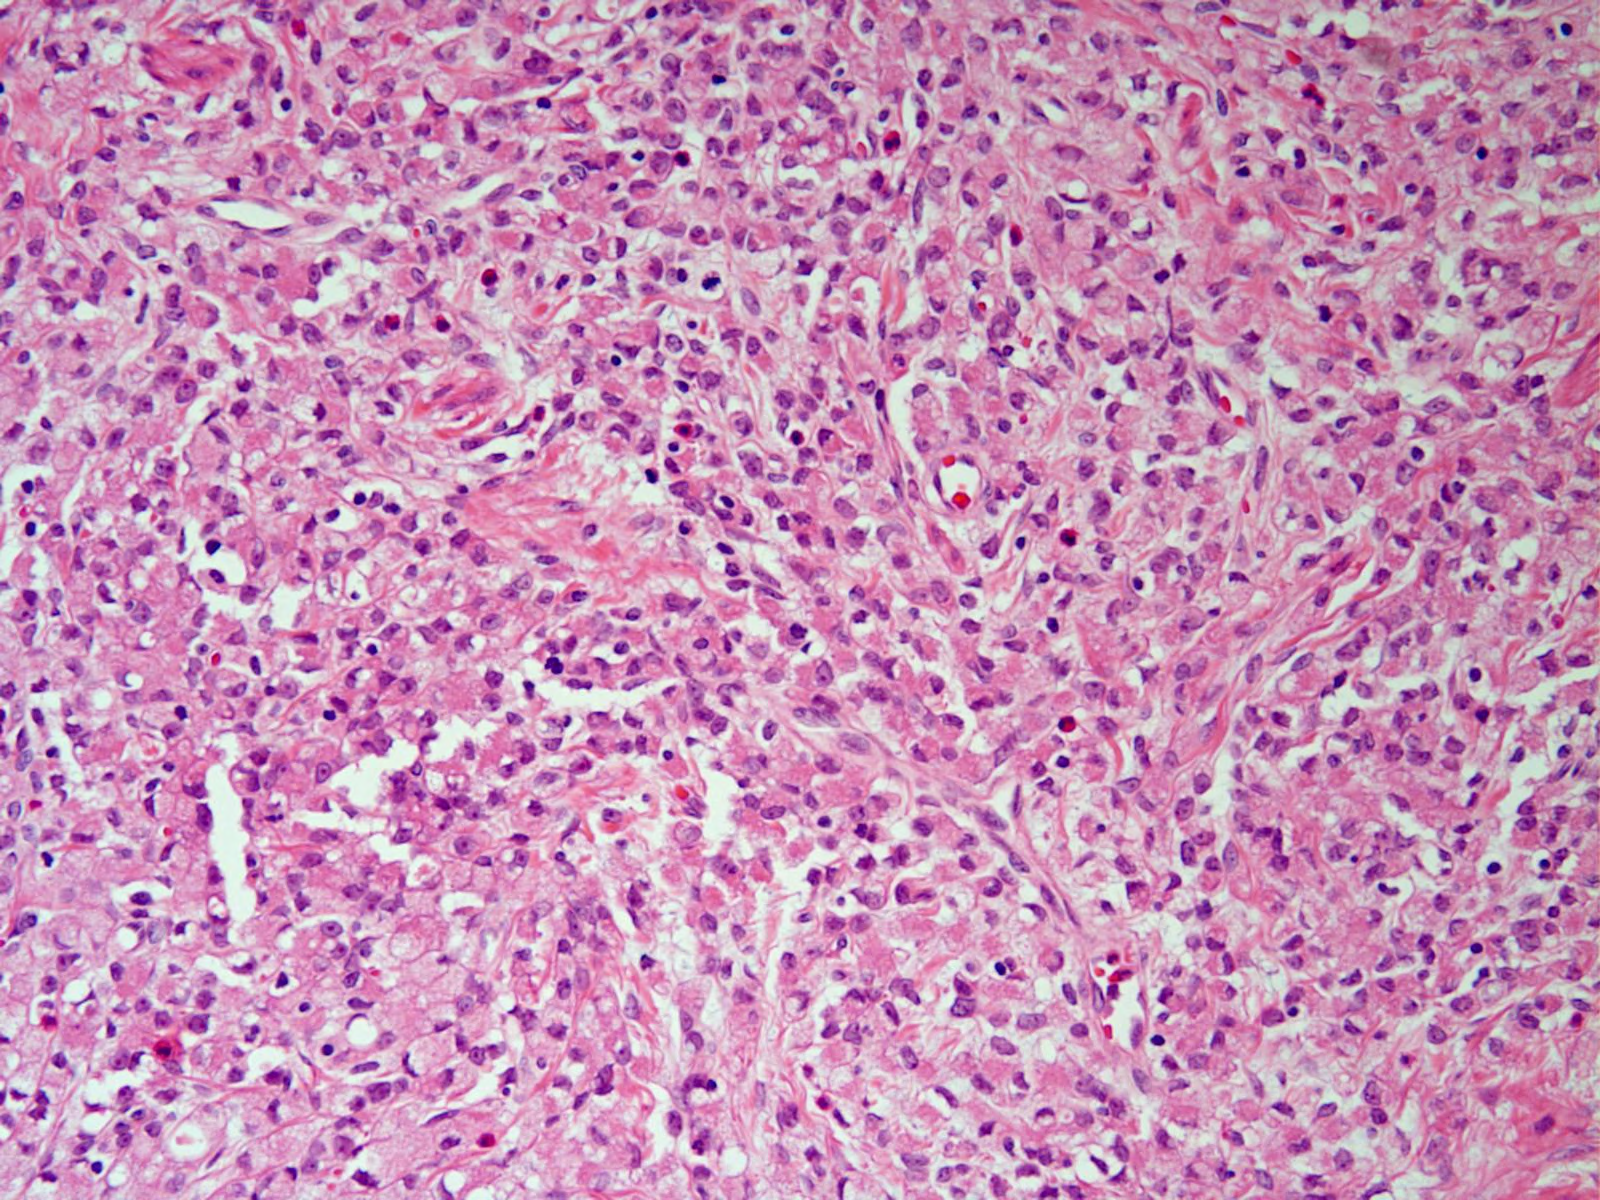
Single-field H&E photomicrograph — covering about 0.8 x 0.6 mm, FFPE section, sample: primary tumour, stomach. Patient: female, age at initial diagnosis 53 years.
Pathologic diagnosis: Adenocarcinoma, NOS (cardia, NOS).